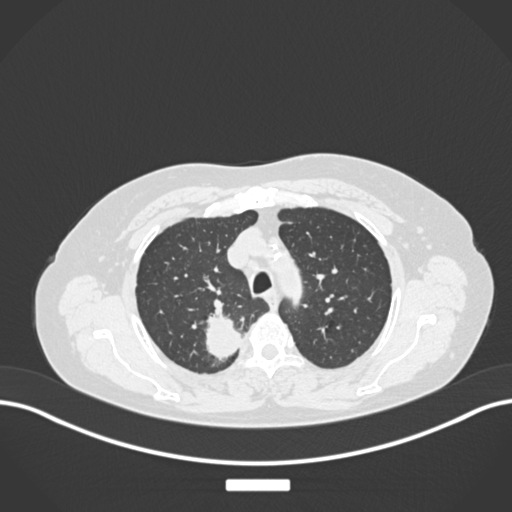
Chest CT, one axial slice. Reconstruction kernel B30f. Lung window (W 1500 / L -600 HU). 1 mm slice thickness. 512 × 512 image matrix. Female patient, age 62 years. Case-level facts recorded for this patient, not image findings: clinical TNM (as recorded): T1c N1 M0.
Structures marked on this image (rectangle marked by the reading radiologist):
- lung tumour (recorded histology: squamous cell carcinoma): box from (x=202, y=301) to (x=247, y=363) px